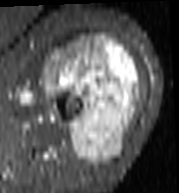
MRI of an extremity soft-tissue mass, one axial slice; position 65 of 103 along the scan axis; STIR; MR volume resampled by the dataset authors to the PET/CT grid (not the native acquisition matrix); 3.27 mm slice thickness; 179 × 193 image matrix, field of view 175 × 188 mm. Female patient. From the clinical record (not read from this slice): histological type: undifferentiated – high grade; grade: high; site of the primary tumour: left thigh.
Outlined on this slice (expert contour drawn on MRI and transferred to this co-registered scan by the dataset authors):
- gross tumour volume including surrounding oedema: box from (x=43, y=35) to (x=142, y=166) px
- gross tumour volume (mass): (x=43, y=35)–(x=140, y=166)